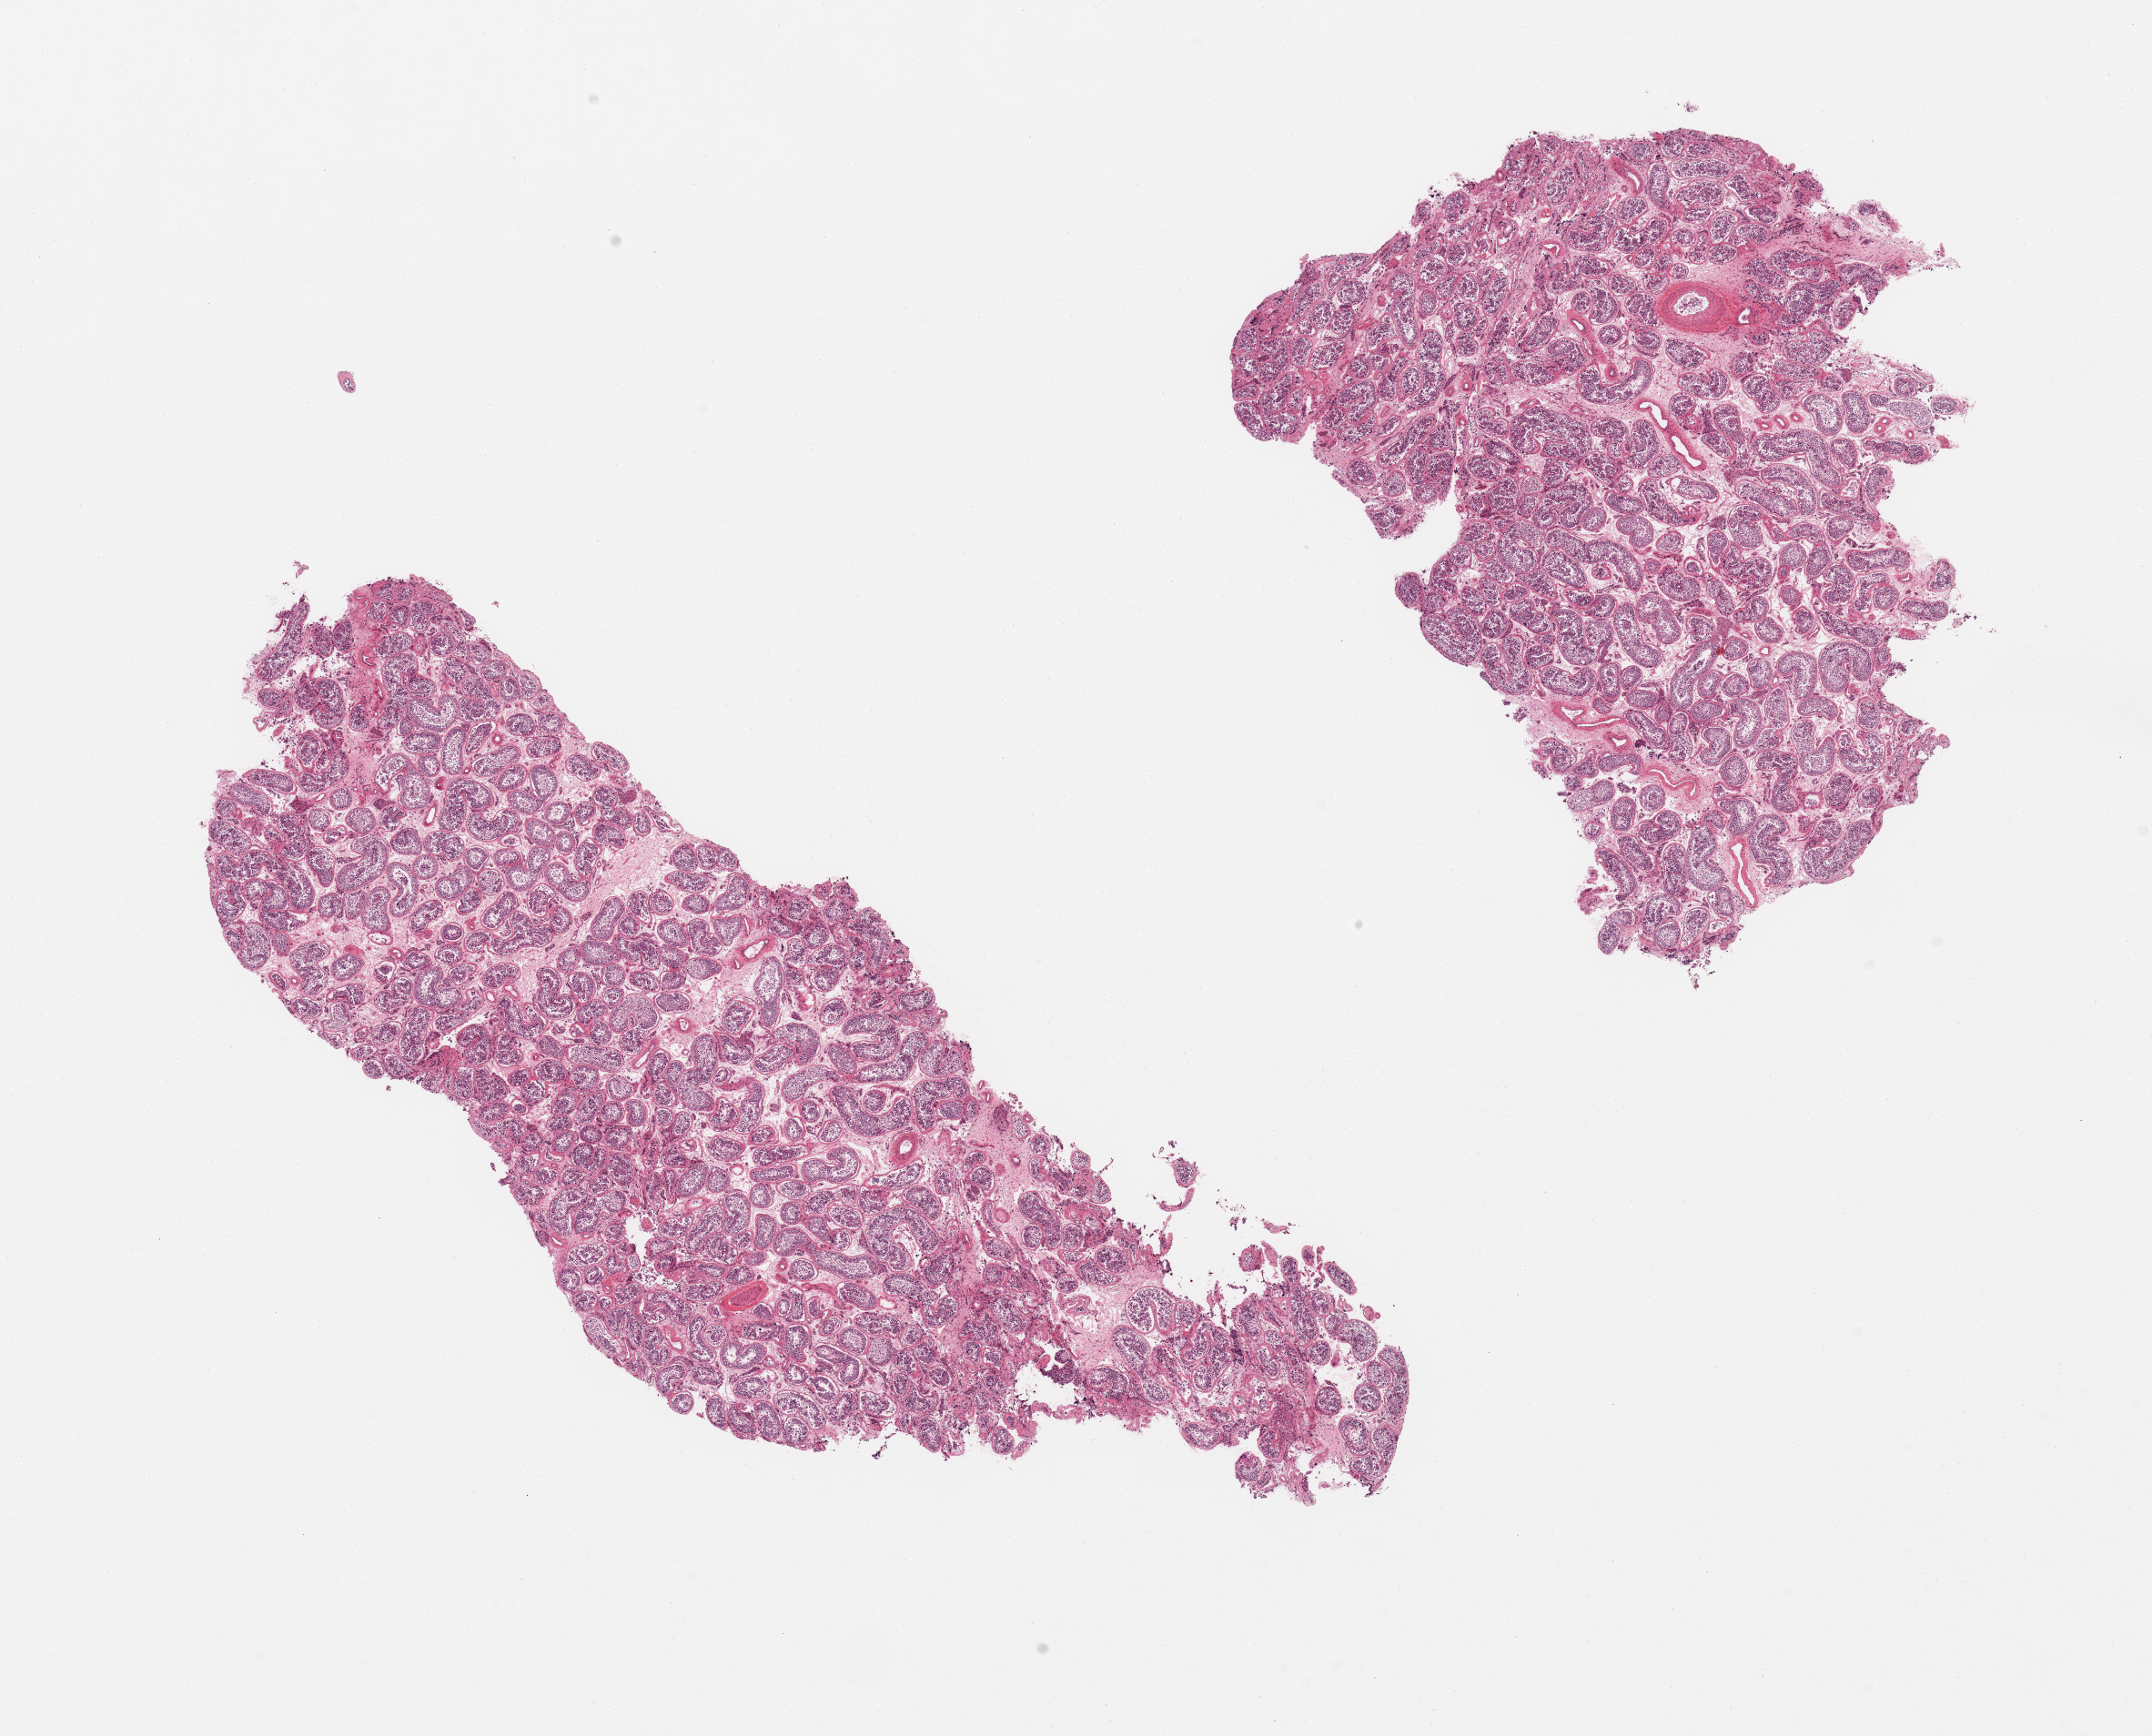
Whole-slide image, hematoxylin and eosin (H&E) stain, shown as a low-resolution overview of the whole scanned area (about 18.7 x 15.1 mm), PAXgene-fixed, paraffin-embedded tissue, section of testis (target tissue), tissue donor sample. Donor: male.
Pathologist's review note for this sample: 2 pieces; spermatogenesis.